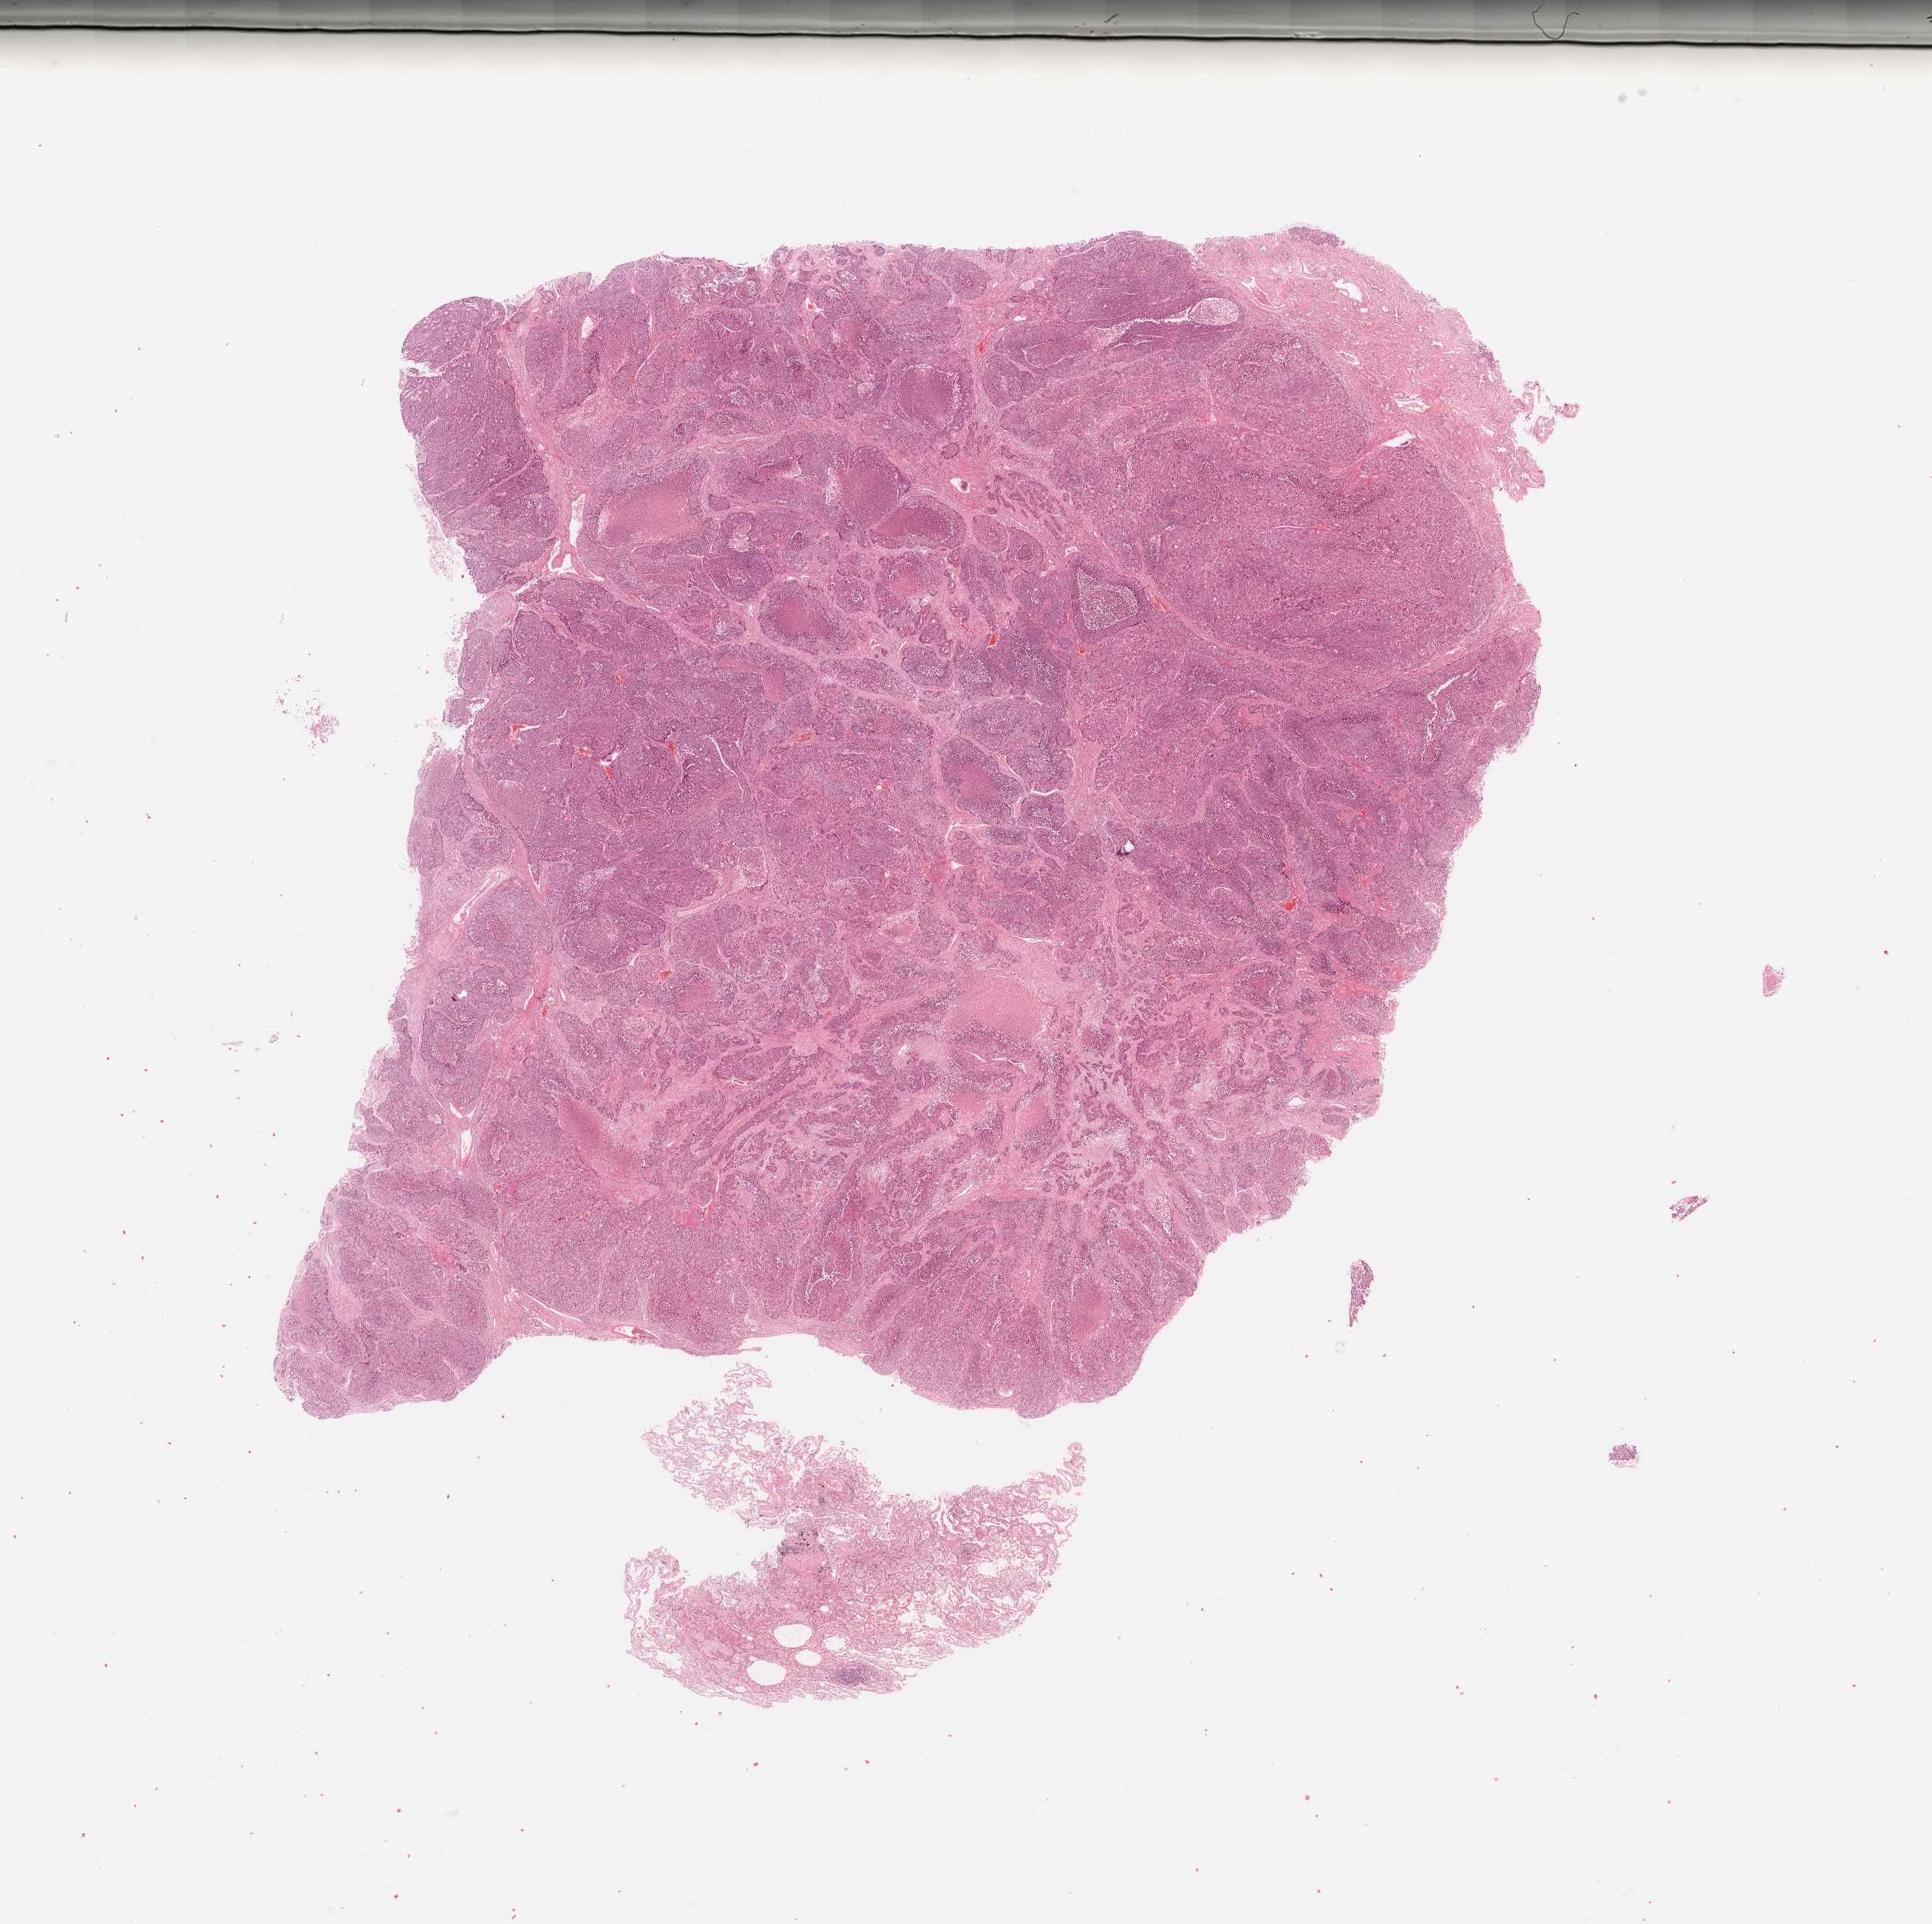
Digitized H&E tissue section (whole slide), a low-resolution overview of the entire scanned area, about 20.7 x 20.6 mm (slide scanned at 20x). Tumour tissue sample, lung. Patient: male, age 58 years. Histologic grade: G3 (poorly differentiated).
Histologic diagnosis: Adenocarcinoma, NOS. AJCC pathologic stage: IB.